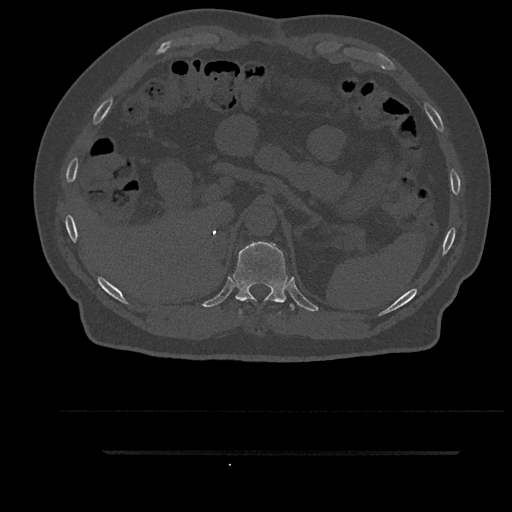
CT including the spine, one axial slice. Position 322 of 797 along the scan axis. Bone window (W 1800 / L 400 HU). 512 × 512 image matrix. Male patient, age 63 years. From the clinical record (not read from this slice): primary cancer: renal.
Outlined on this slice (semi-automatic segmentation, software-assisted and operator-edited):
- T11 vertebra: bounding box [x1, y1, x2, y2] px = [233, 241, 294, 314]